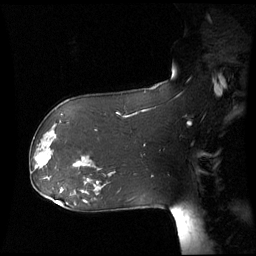
Breast MRI (dynamic contrast-enhanced), one sagittal slice. Slice 39 of 60 in the series (ordered by position). Dynamic contrast-enhanced series, image 2 of 3 at this slice position (ordered by acquisition). 1.5 T. TE 4.2 ms, TR 8.9 ms. 256 × 256 image matrix, field of view 280 × 280 mm. Female patient, age 61 years. From the clinical record (not read from this slice): setting: breast cancer imaged before/during neoadjuvant chemotherapy; receptor status: HR-positive, HER2-negative.
Outlined on this slice (semi-automatically segmented with operator editing):
- analysis volume of interest (the breast-tissue region the enhancement analysis was run in; not a lesion): box from (x=30, y=142) to (x=53, y=175) px
- tumour enhancement mask (voxels above the 70 % enhancement threshold inside the analysis volume of interest): (x=36, y=154)–(x=49, y=169)